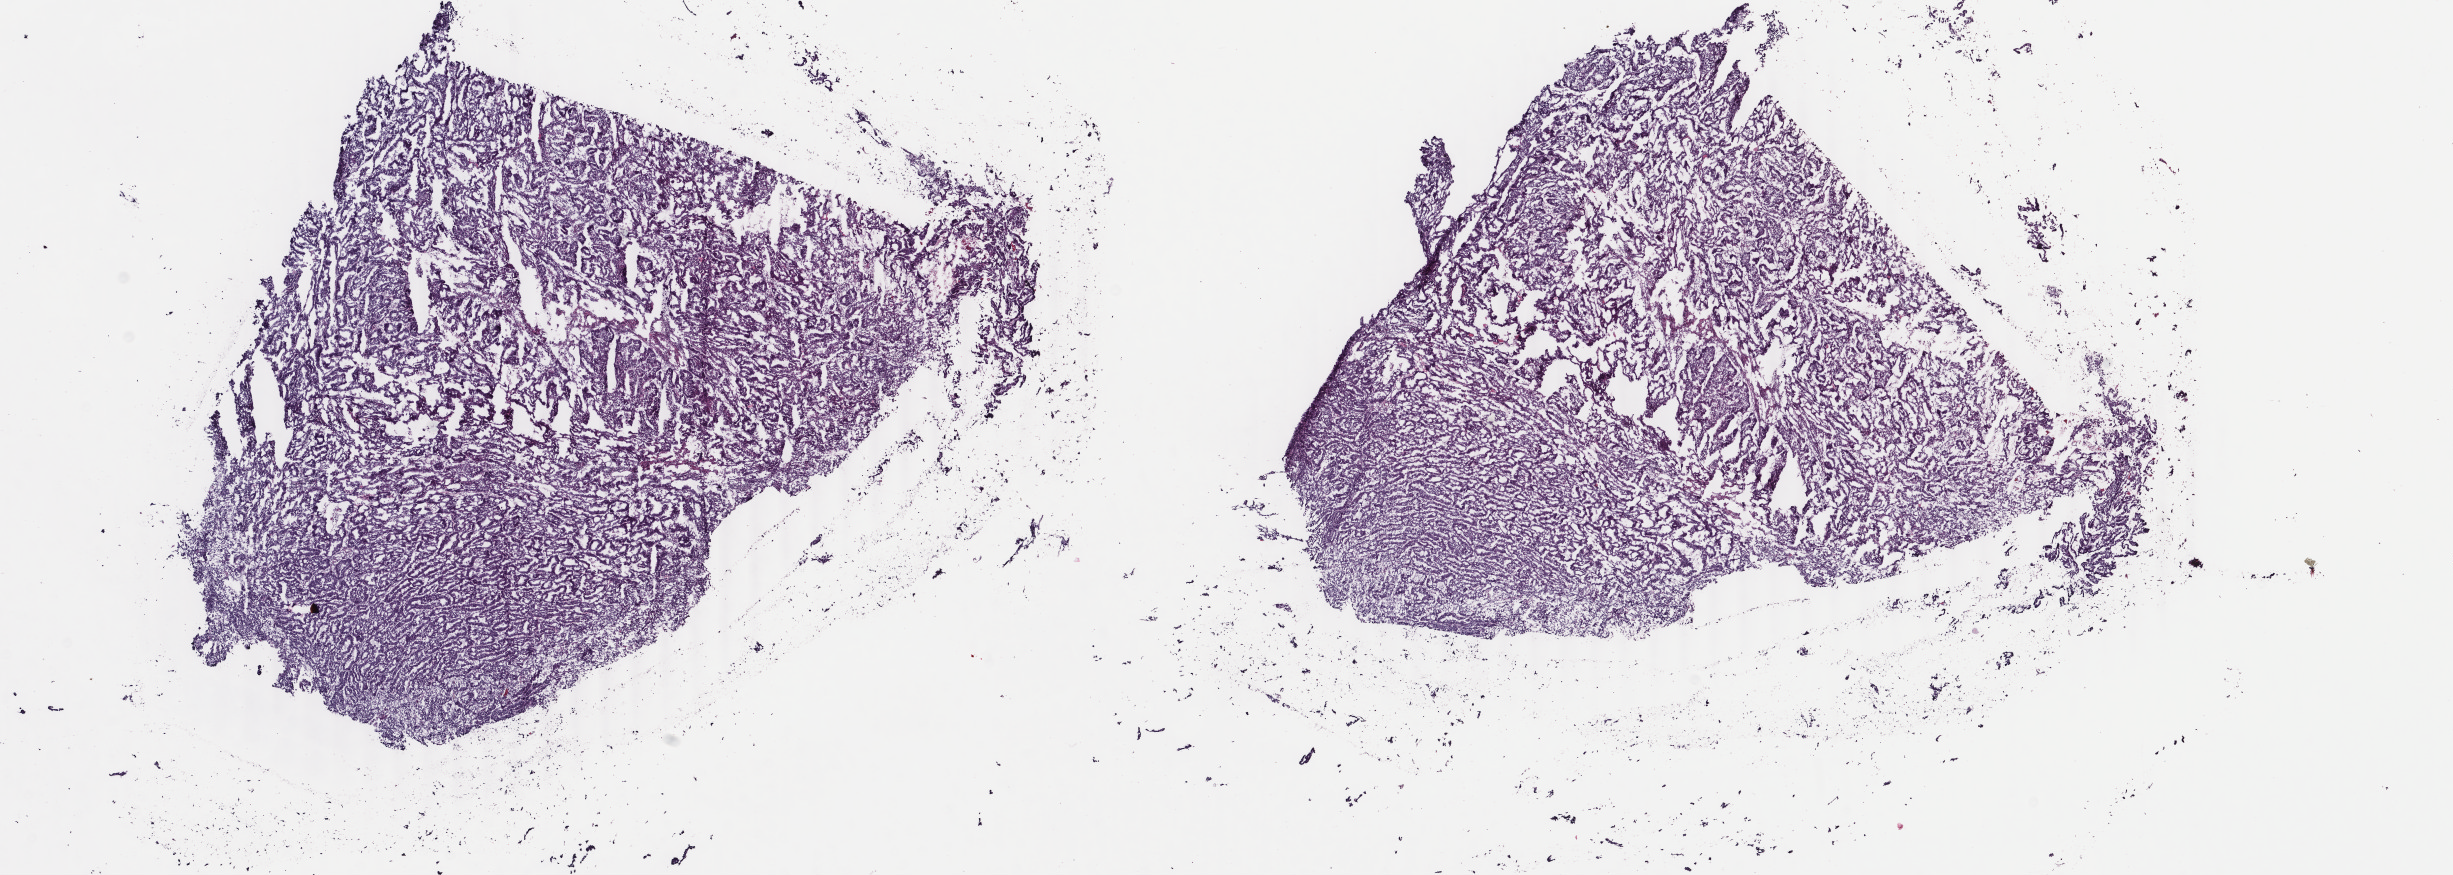
Digitized Hematoxylin and eosin (H&E) stained tissue section (whole slide), whole scanned area (about 19.5 x 7.0 mm) shown as a low-resolution overview; frozen section; sample: primary tumour, uterus. Female, age 55 years at initial diagnosis. Histologic grade: G2 (moderately differentiated). Slide review estimates, as recorded: tumour cells 99%, tumour nuclei 99%, normal cells 0%, stromal cells 0%, necrosis 1%. Inflammatory infiltration, as recorded: lymphocyte infiltration 2%, monocyte infiltration 6%, neutrophil infiltration 1%.
Histologic diagnosis: Endometrioid adenocarcinoma, NOS (endometrium). FIGO stage: IA.